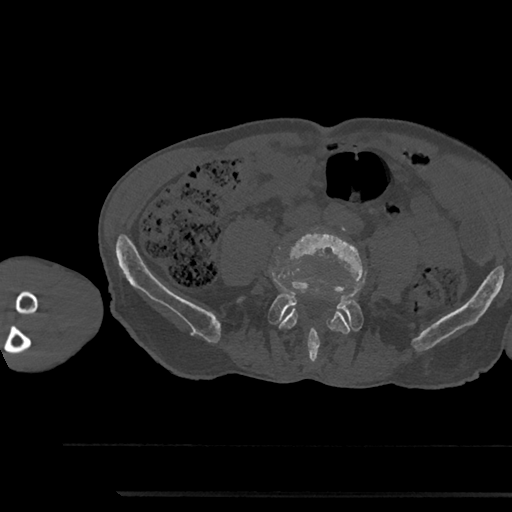
CT including the spine, one axial slice. Slice 377 of 797 in the series (ordered by position). Bone window (W 1800 / L 400 HU). 512 × 512 image matrix. Patient: male, 79 years. From the clinical record (not read from this slice): primary cancer: prostate.
Annotated regions visible in this slice (semi-automatic segmentation, software-assisted and operator-edited):
- L4 vertebra: bounding box (x1, y1, x2, y2) in pixels: (278, 228, 364, 334)
- L5 vertebra: (243, 282, 362, 360)